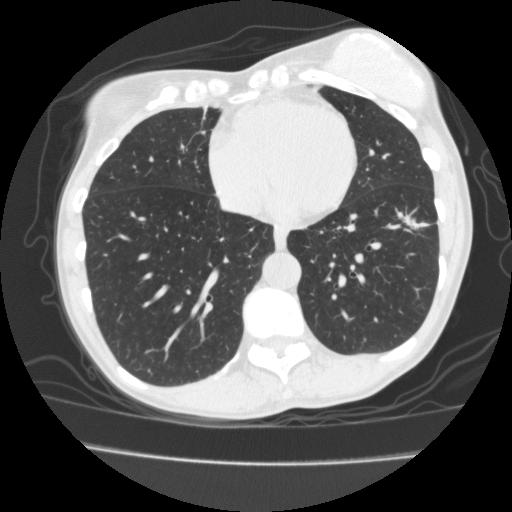
Low-dose screening chest CT, one axial slice; slice 58 of 171 in the series (ordered by position); reconstruction kernel FC10; 120 kVp; lung window (W 1500 / L -600 HU); 2 mm slice thickness; 512 × 512 image matrix, field of view 339 × 339 mm.
Outlined on this slice (outlined manually by an expert reader):
- lesion 1 (tumor, lower lobe of left lung): bounding box [x1, y1, x2, y2] px = [406, 218, 420, 228]